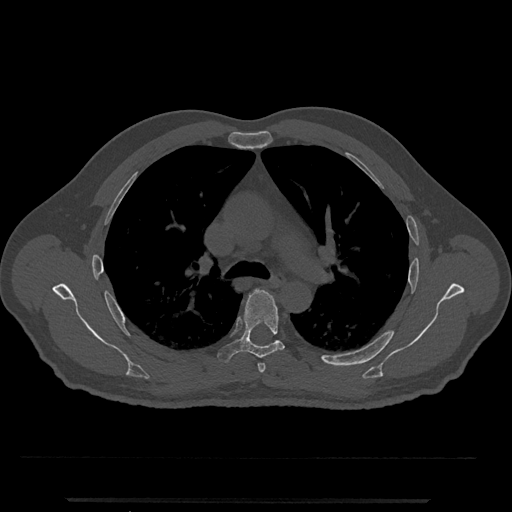
CT including the spine, one axial slice; position 796 of 797 along the scan axis; bone window (W 1800 / L 400 HU); 0.5 mm slice thickness; 512 × 512 image matrix. Male patient, age 63 years. From the clinical record (not read from this slice): primary cancer: prostate.
Annotated regions visible in this slice (semi-automatically segmented with operator editing):
- T5 vertebra: box from (x=217, y=290) to (x=285, y=363) px
- T6 vertebra: (x=272, y=341)–(x=277, y=344)